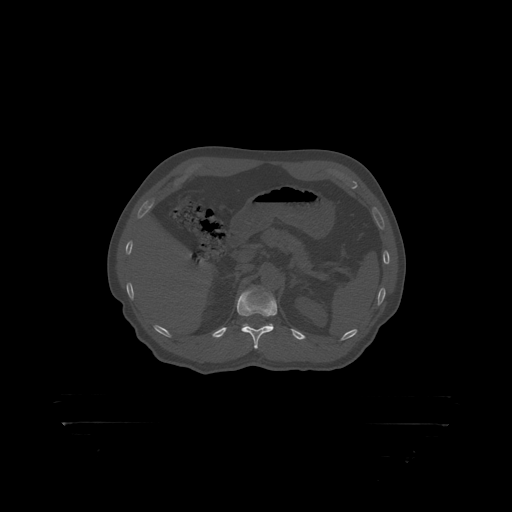
CT including the spine, one axial slice; position 346 of 399 along the scan axis; bone window (W 1800 / L 400 HU); 1.25 mm slice thickness; 512 × 512 image matrix. Male patient, age 46 years. From the clinical record (not read from this slice): primary cancer: skin.
Outlined on this slice (semi-automatically segmented with operator editing):
- T12 vertebra: box from (x=237, y=288) to (x=277, y=317) px